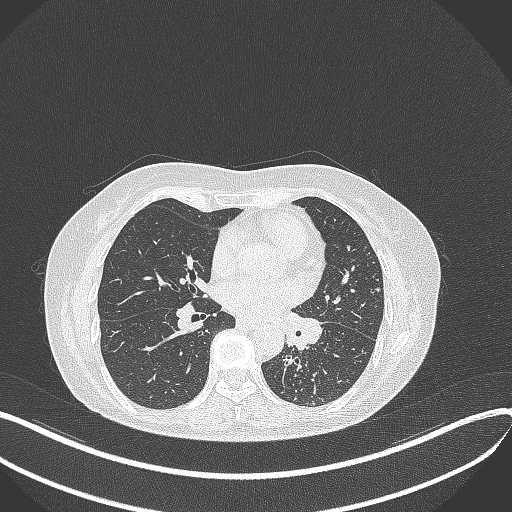
Chest CT, one axial slice; position 197 of 429 along the scan axis; reconstruction kernel B70f; 100 kVp; lung window (W 1500 / L -600 HU); 1 mm slice thickness; 512 × 512 image matrix, field of view 400 × 400 mm. Female patient, age 63 years. From the clinical record (not read from this slice): clinical TNM (as recorded): T1b N0 M0; histopathological grade: G2-3.
Structures marked on this image (rectangle marked by the reading radiologist):
- lung tumour (recorded histology: adenocarcinoma): bounding box [x1, y1, x2, y2] px = [282, 307, 323, 350]